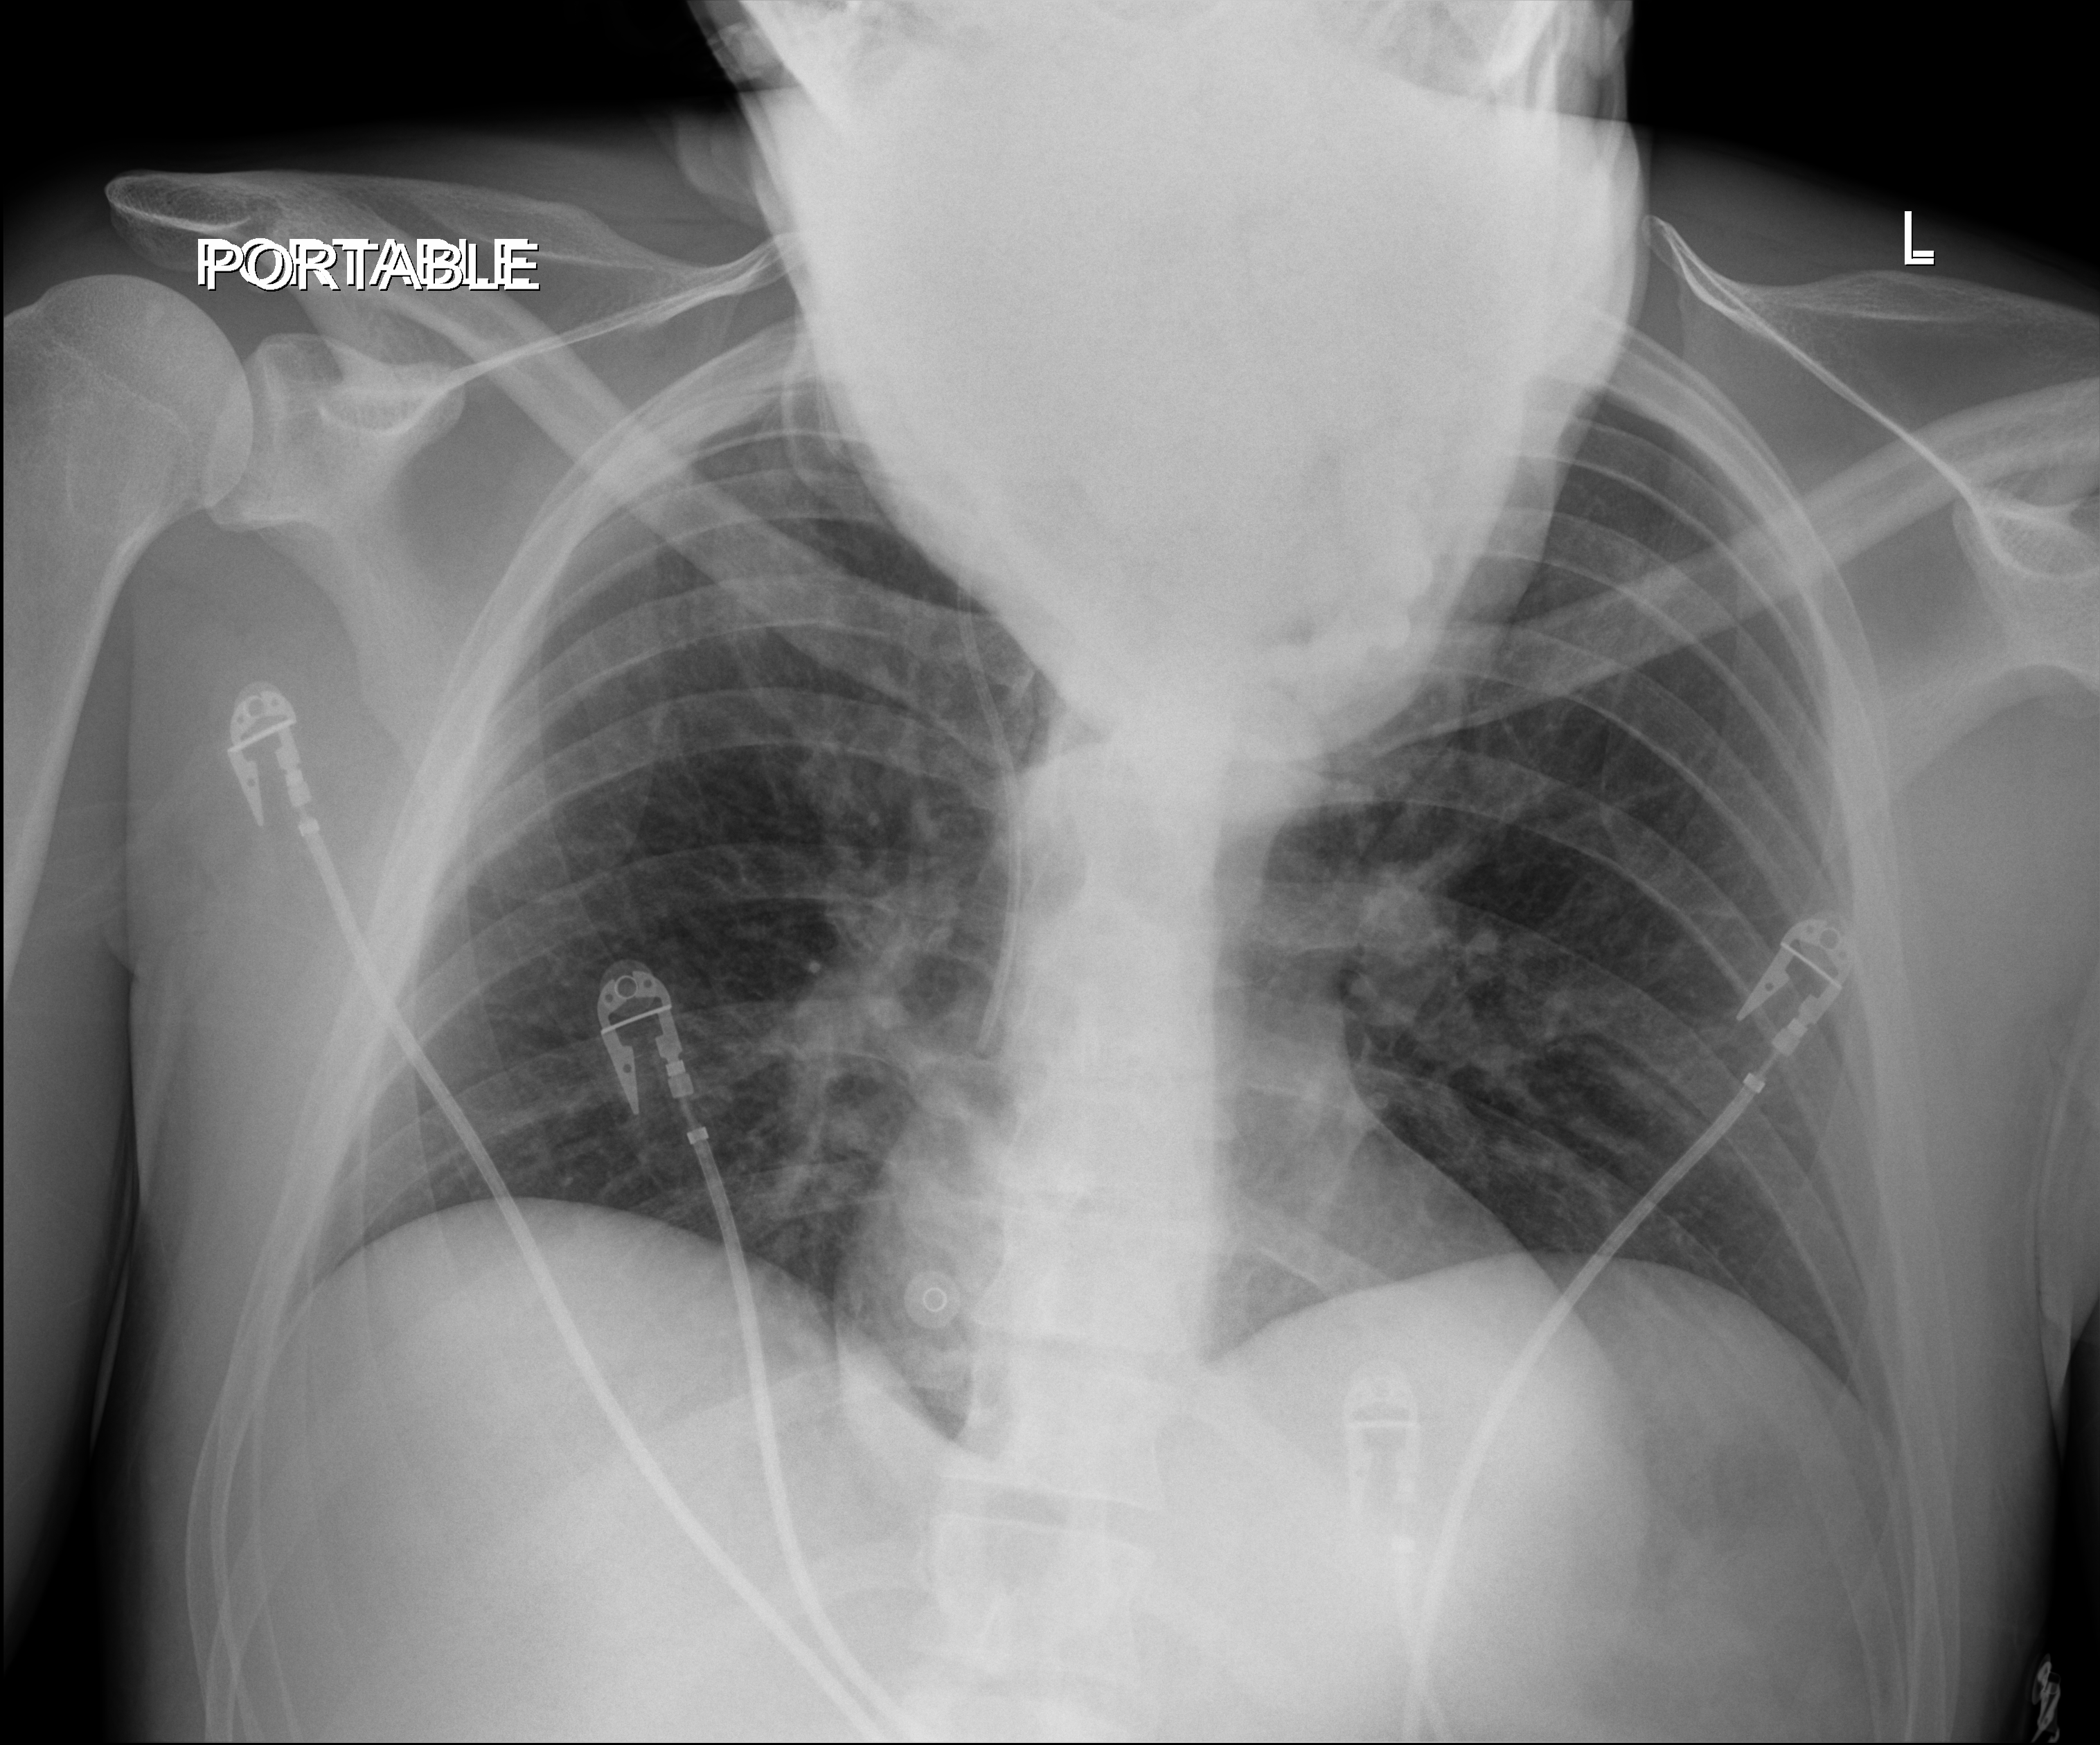
Portable chest radiograph. Patient hospitalised with COVID-19; male, aged 18–59 years.
From the hospital-stay record, not from the radiograph (when in the stay this image was taken is not recorded): admitted to intensive care during this hospital stay: no; mechanically ventilated during this hospital stay: yes.